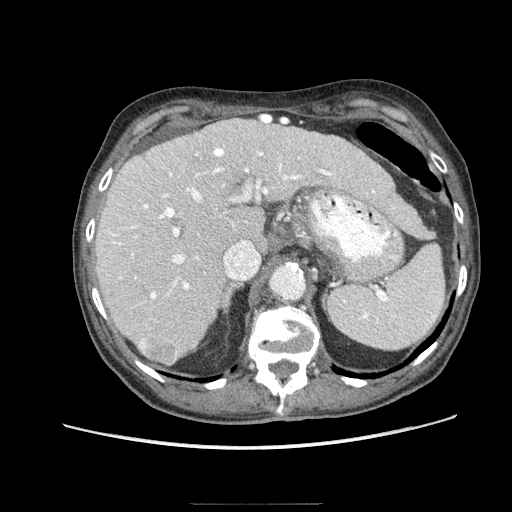
Contrast-enhanced abdominal CT (liver protocol), one axial slice; position 57 of 83 along the scan axis; reconstruction kernel STANDARD; soft-tissue window (W 400 / L 40 HU); 2.5 mm slice thickness; 512 × 512 image matrix, field of view 360 × 360 mm. Case-level facts recorded for this patient, not image findings: diagnosis: hepatocellular carcinoma (patient treated with transarterial chemoembolisation; whether this scan precedes or follows treatment is not stated here); TNM stage (as recorded): Stage-I; Child-Pugh class: A; tumour differentiation: moderately differentiated; tumour nodularity: uninodular.
Annotated regions visible in this slice (semi-automatic segmentation, software-assisted and operator-edited):
- liver parenchyma outside the tumour (the mass and vessels are separate outlines, so this box may not span the whole liver): bounding box (x1, y1, x2, y2) in pixels: (96, 118, 408, 364)
- mass: (137, 333, 178, 366)
- liver vessels: (108, 120, 394, 299)